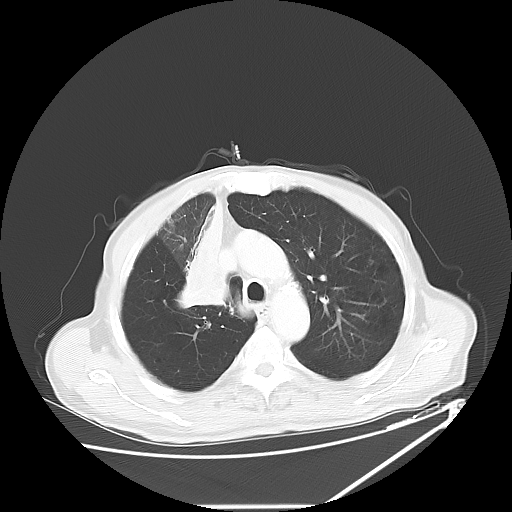
Chest CT, one axial slice; slice 45 of 60 in the series (ordered by position); reconstruction kernel LUNG; 120 kVp; lung window (W 1500 / L -600 HU); 5 mm slice thickness; 512 × 512 image matrix, field of view 410 × 410 mm. Patient: male, 73 years. From the clinical record (not read from this slice): clinical TNM (as recorded): T2a N1 M0.
Outlined on this slice (rectangle marked by the reading radiologist):
- lung tumour (recorded histology: squamous cell carcinoma): bounding box [x1, y1, x2, y2] px = [169, 180, 246, 327]